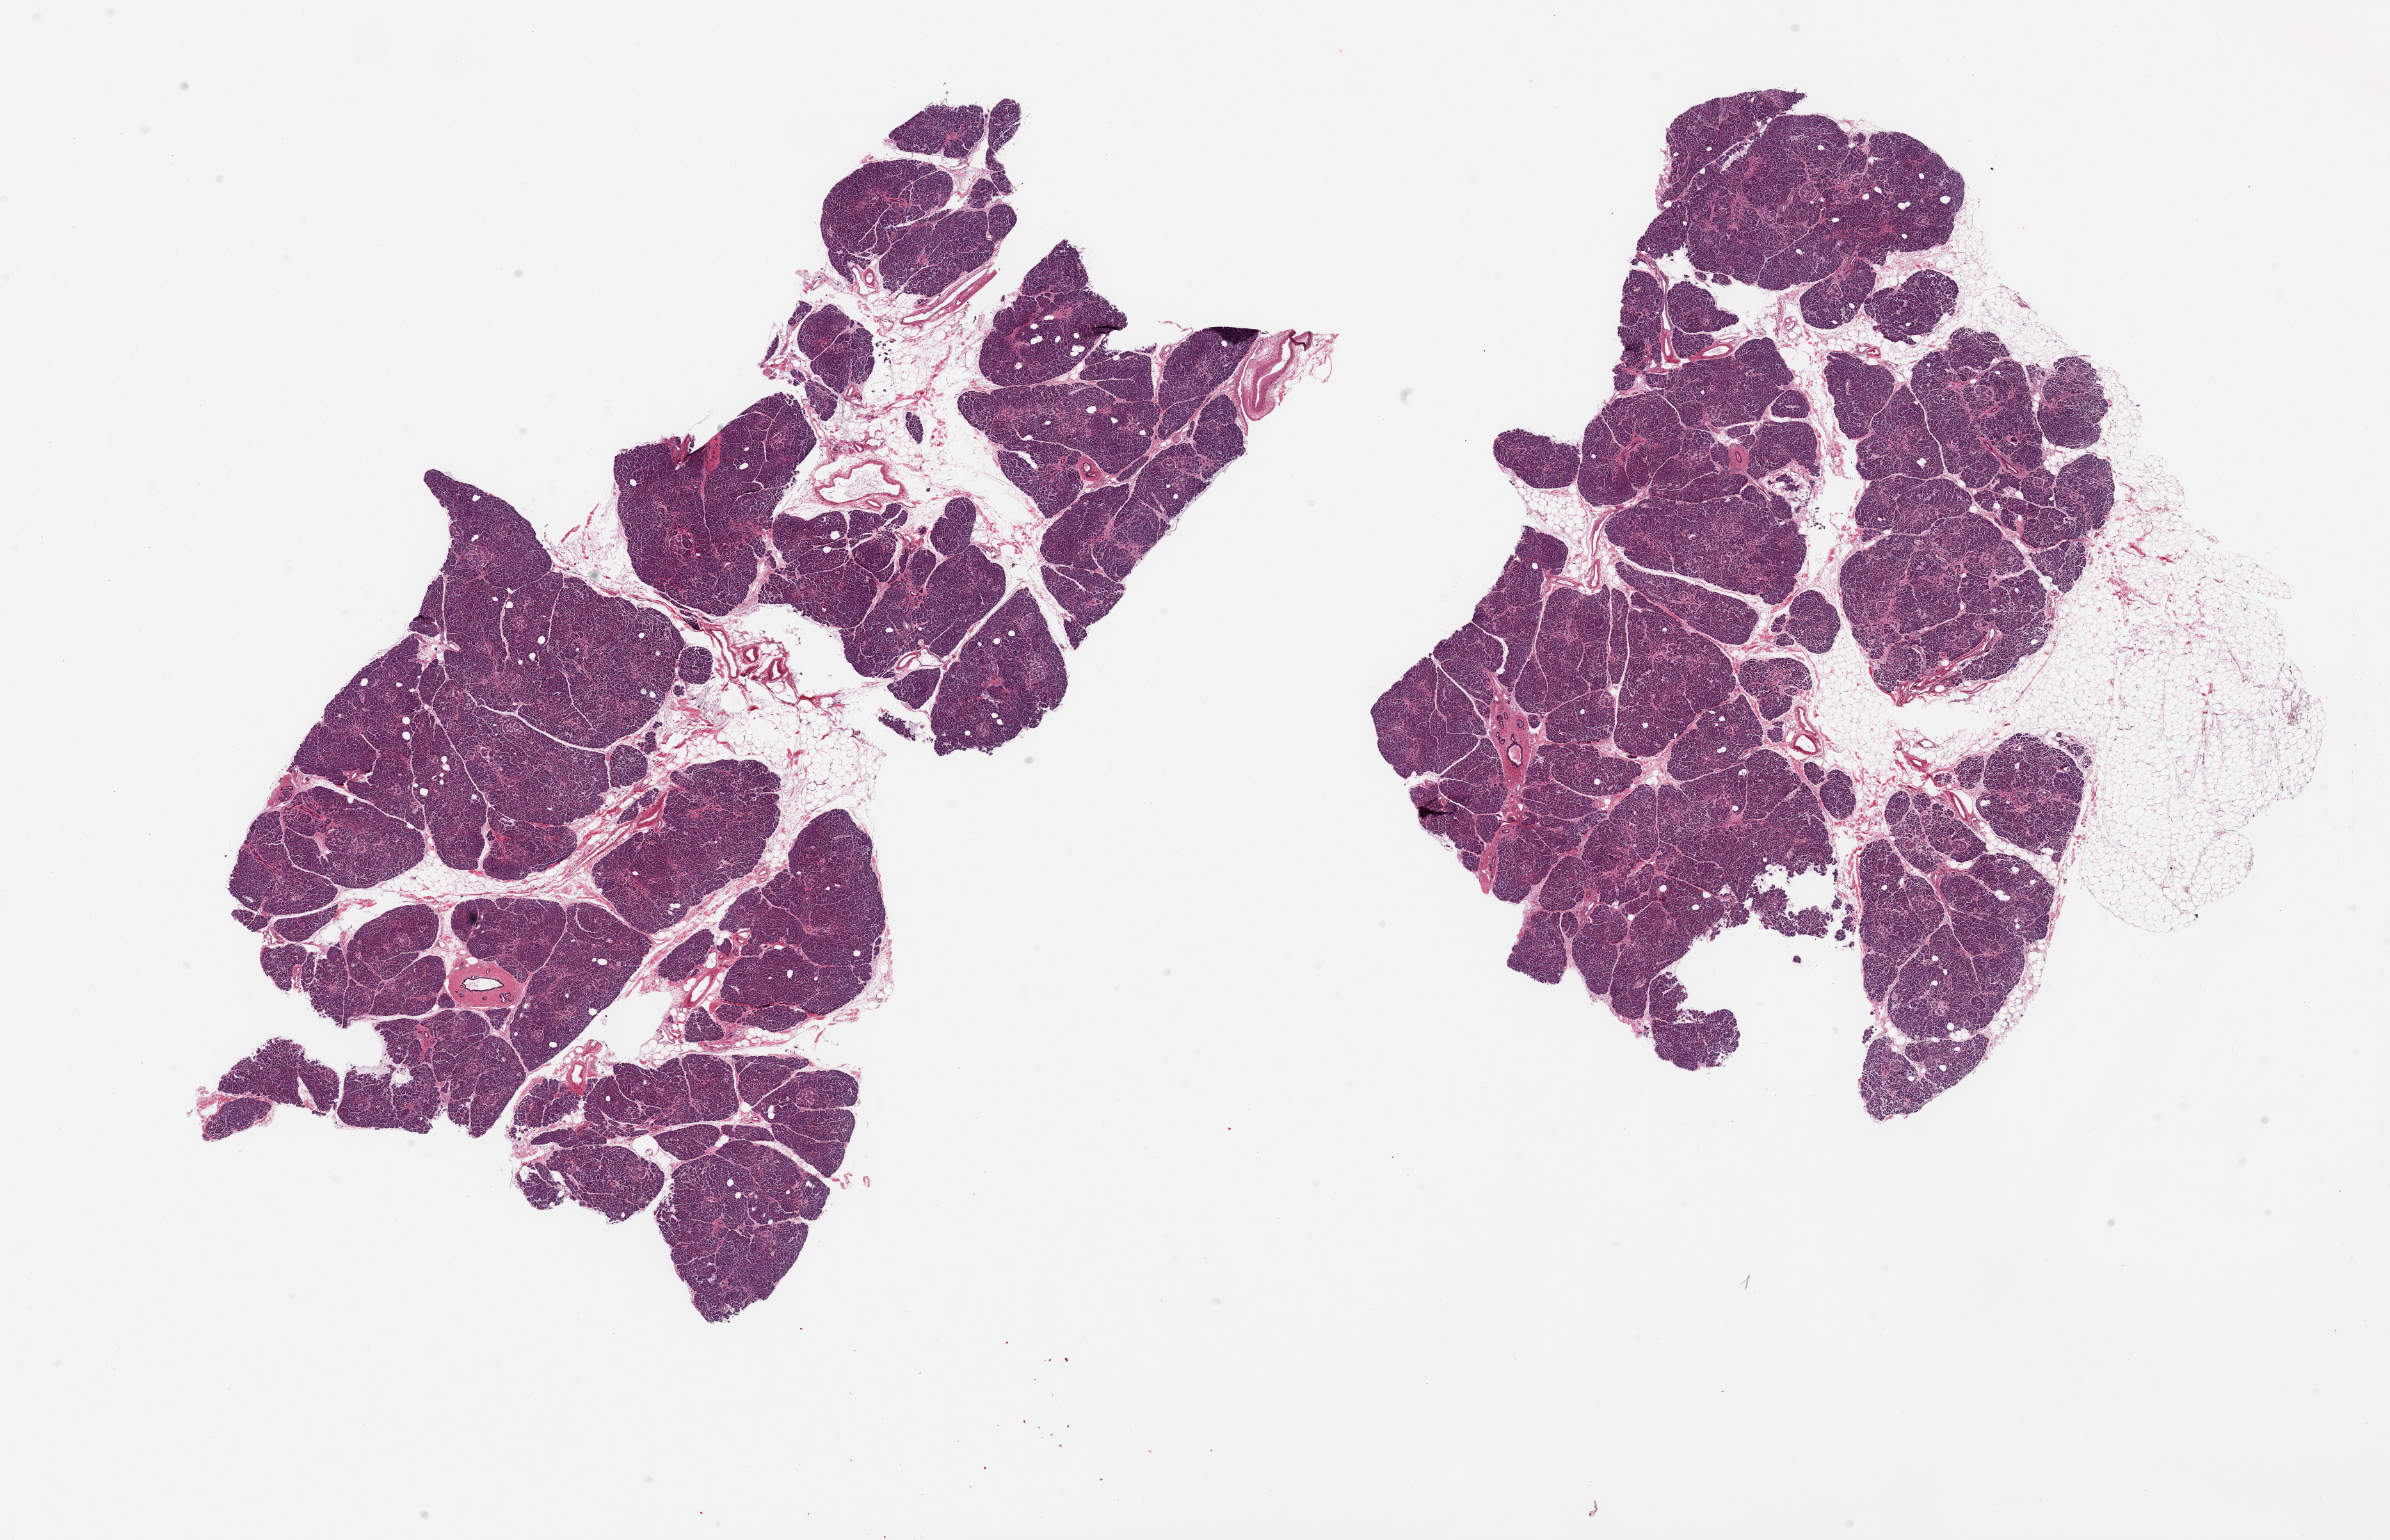
Whole-slide image, H&E stain — shown as a low-resolution overview of the whole scanned area (about 29.5 x 19.0 mm, slide scanned at 20x). PAXgene-fixed, paraffin-embedded tissue. Section of pancreas (target tissue). Tissue donor sample. Female donor.
Review note (as recorded): 2 pieces 20 & 10% internal & external fat.